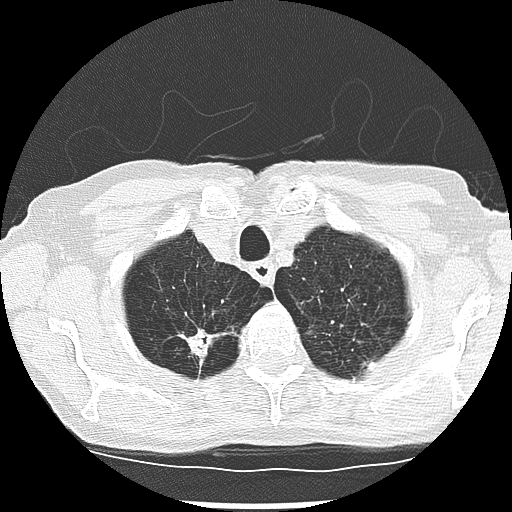
Low-dose screening chest CT, one axial slice. Position 237 of 265 along the scan axis. Reconstruction kernel LUNG. Lung window (W 1500 / L -600 HU). 512 × 512 image matrix.
Outlined on this slice (manually delineated by an expert):
- lesion 2 (tumor, upper lobe of right lung): bounding box <180,329,217,362> (left, top, right, bottom; pixels)